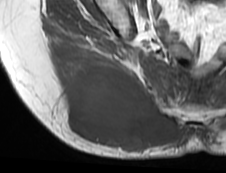
MRI of an extremity soft-tissue mass, one axial slice. Position 41 of 73 along the scan axis. MR volume resampled by the dataset authors to the PET/CT grid (not the native acquisition matrix). 226 × 173 image matrix, field of view 221 × 169 mm. Female patient. From the clinical record (not read from this slice): histological type: spindle cell suggestive of myxofibrosarcoma; grade: intermediate; site of the primary tumour: right buttock.
Annotated regions visible in this slice (expert contour drawn on MRI and transferred to this co-registered scan by the dataset authors):
- gross tumour volume (mass): bounding box (x1, y1, x2, y2) in pixels: (61, 65, 187, 151)